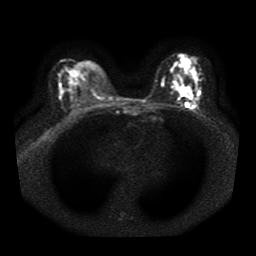
Breast MRI, one axial slice. Diffusion-weighted series; image 2 of 4 stored at this slice position (different b-values; order by instance number). 1.5 T. 5 mm slice thickness. 256 × 256 image matrix, field of view 330 × 330 mm. Female patient.
Structures marked on this image (outlined manually by an expert reader):
- tumour on diffusion-weighted imaging: box from (x=181, y=87) to (x=193, y=98) px